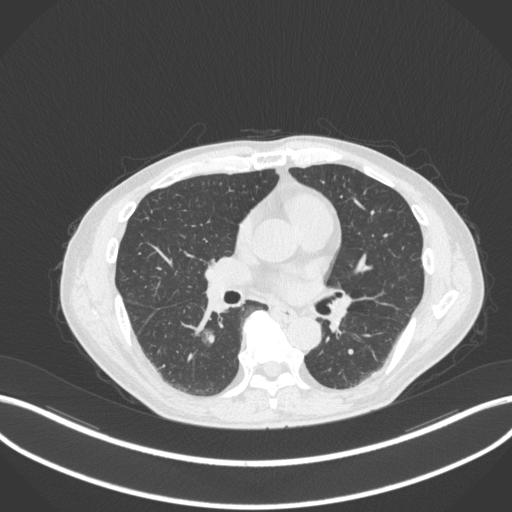
Chest CT, one axial slice; position 163 of 324 along the scan axis; lung window (W 1500 / L -600 HU); 1 mm slice thickness; 512 × 512 image matrix, field of view 400 × 400 mm. Male patient, age 61 years. From the clinical record (not read from this slice): clinical TNM (as recorded): T1c N0 M0.
Annotated regions visible in this slice (rectangle marked by the reading radiologist):
- lung tumour (recorded histology: adenocarcinoma): box from (x=197, y=329) to (x=220, y=352) px